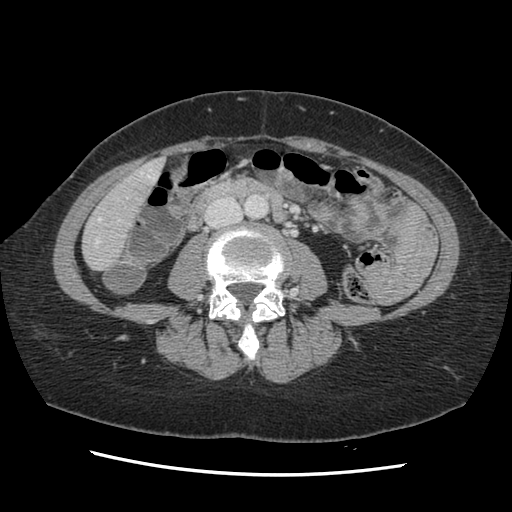
Contrast-enhanced abdominal CT, one axial slice. Position 30 of 141 along the scan axis. 120 kVp. Soft-tissue window (W 400 / L 40 HU). 2.5 mm slice thickness. 512 × 512 image matrix, field of view 330 × 330 mm. Female patient, age 61 years. Case-level facts recorded for this patient, not image findings: diagnosis: colorectal cancer liver metastases, imaged before liver resection; multiple liver metastases: no; largest metastasis: 2.4 cm; disease in both lobes: no.
Outlined on this slice (expert manual segmentation):
- hepatic veins: bounding box <95,170,157,245> (left, top, right, bottom; pixels)
- liver: <84,160,163,270>
- planned liver remnant (the part of the liver to remain after resection): <84,161,162,270>